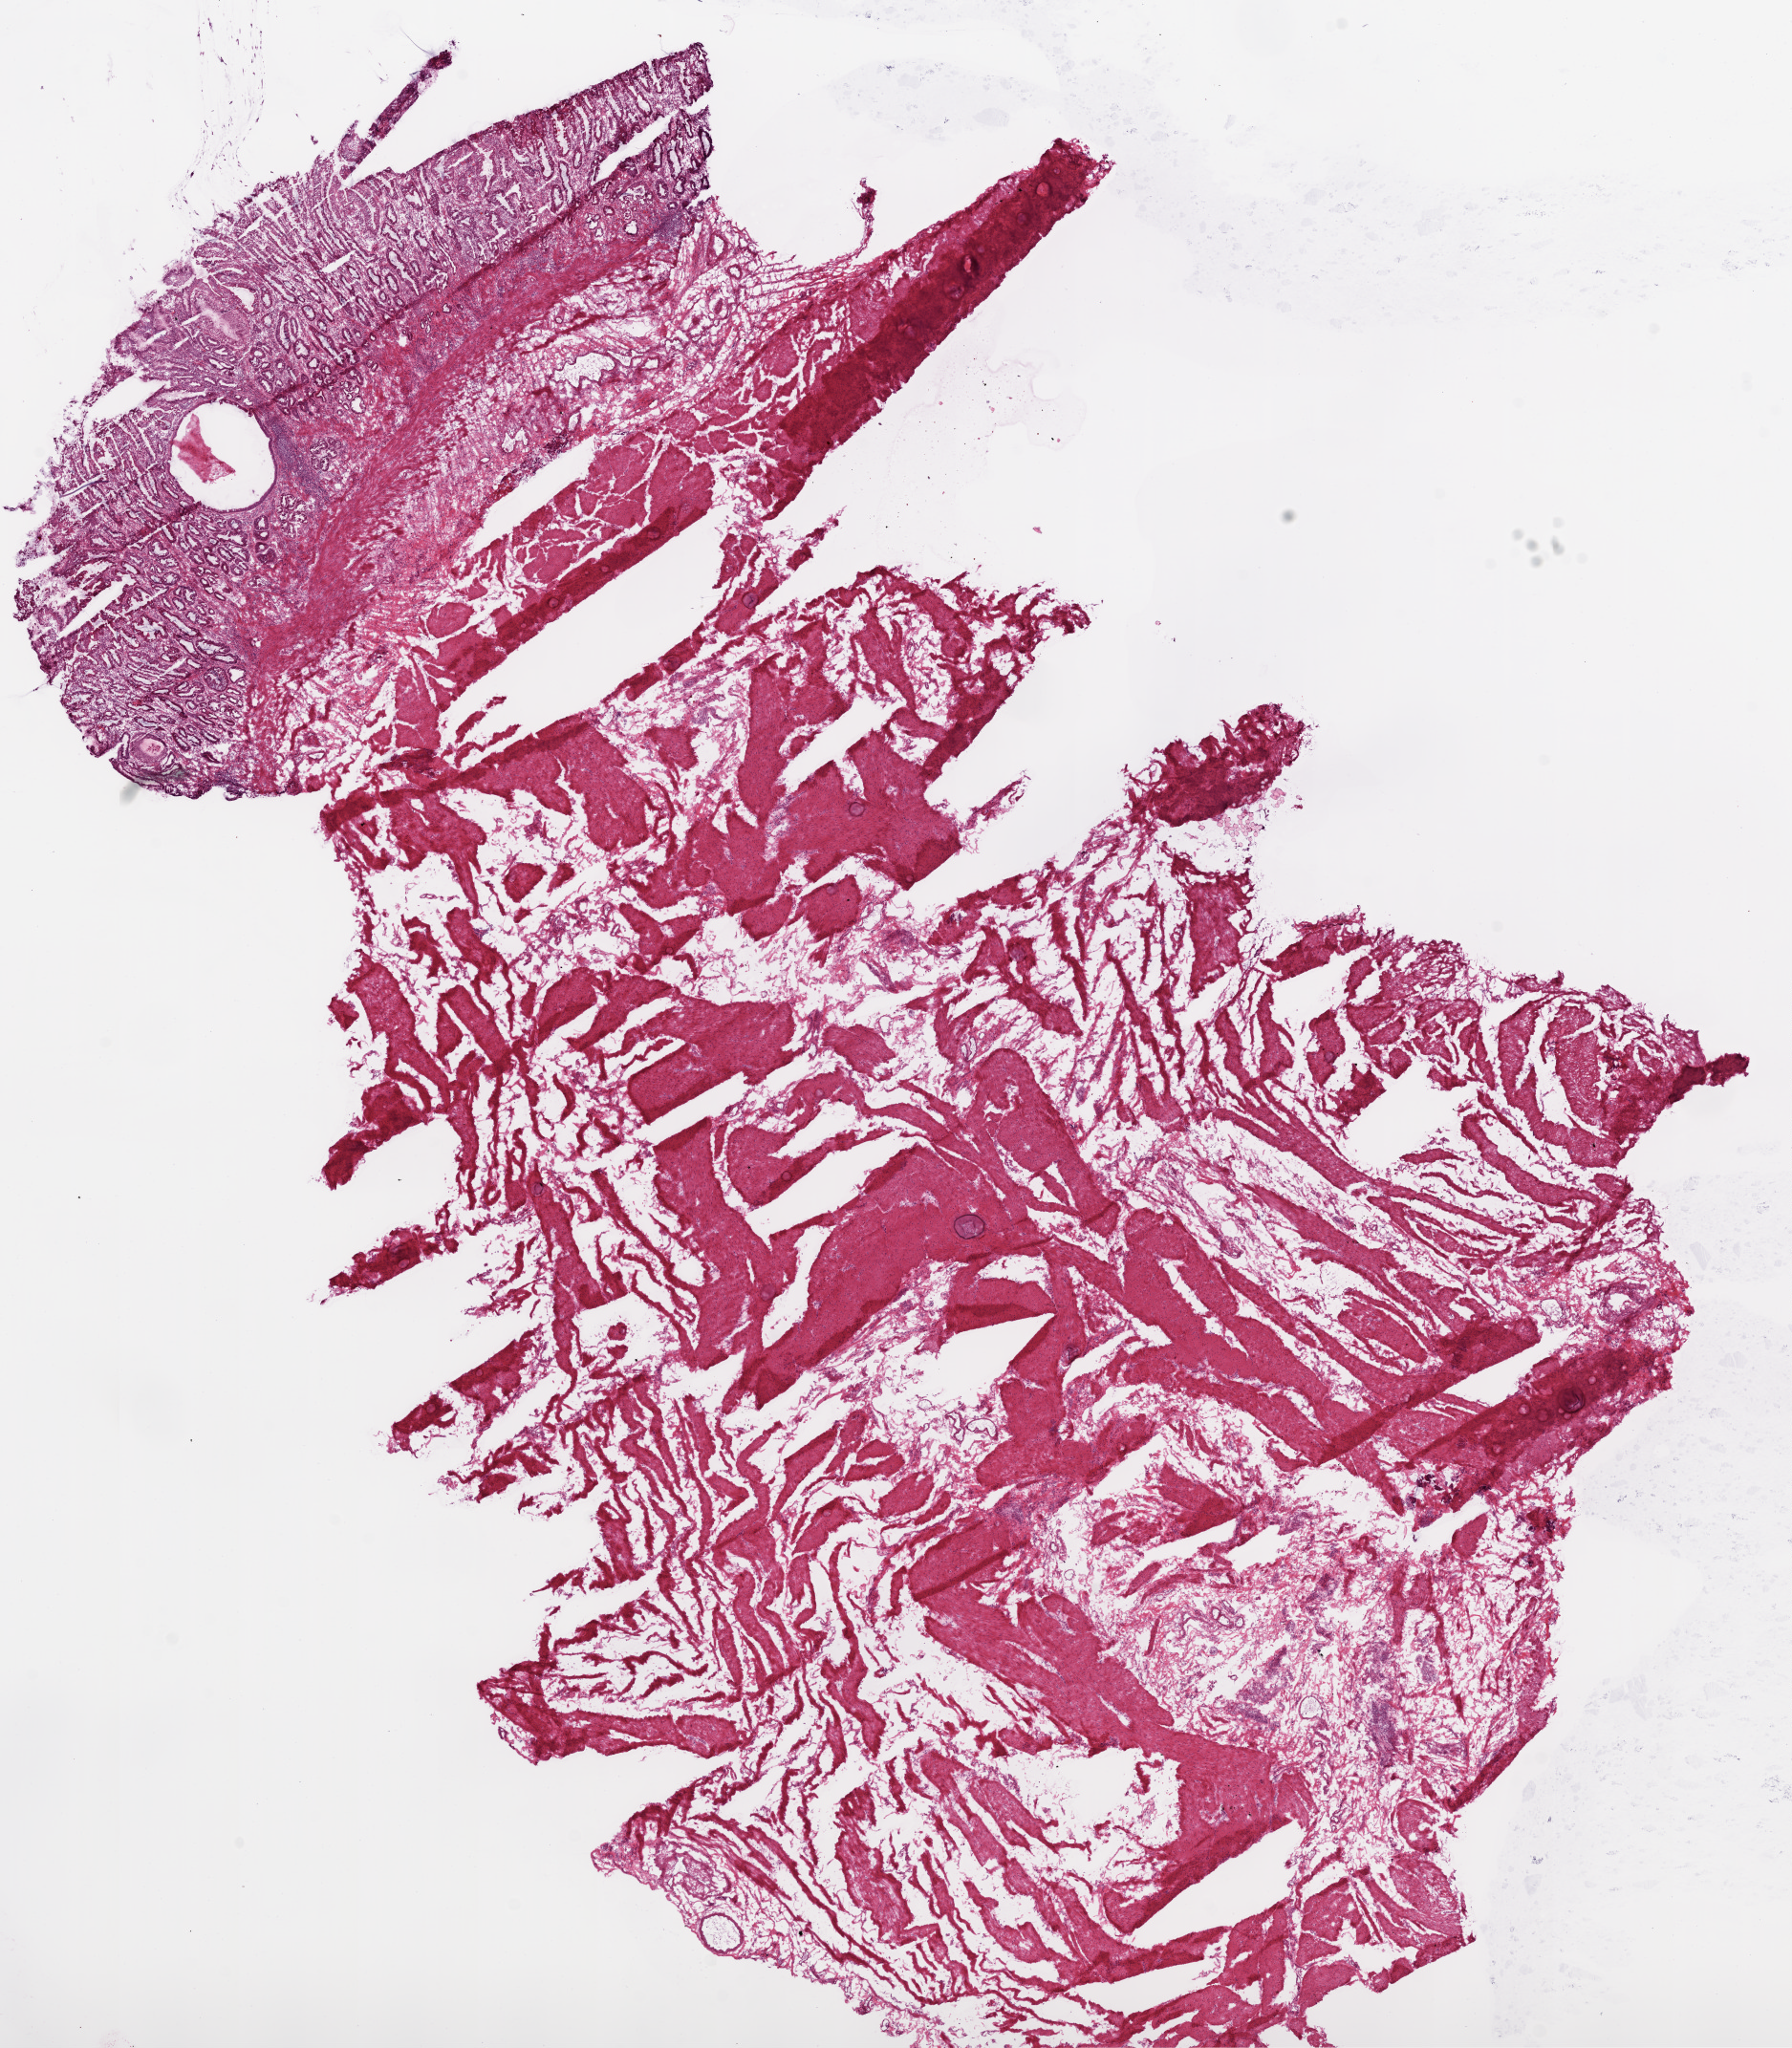
Digitized H&E-stained tissue section (whole slide) — low-resolution overview of the scanned area, about 15.0 x 17.2 mm. Frozen section. Stomach, solid tissue normal (non-tumour tissue) sample. Female, age 78 years at initial diagnosis.
This section: solid tissue normal sample (biorepository sample class). Patient diagnosis: Adenocarcinoma, NOS.